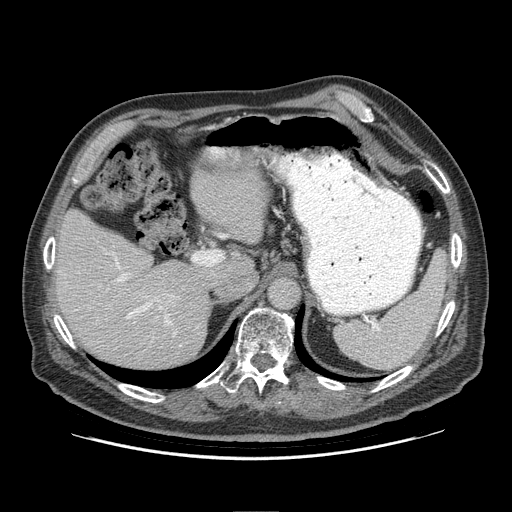
Contrast-enhanced abdominal CT (liver protocol), one axial slice; slice 62 of 95 in the series (ordered by position); reconstruction kernel STANDARD; 140 kVp; soft-tissue window (W 400 / L 40 HU); 512 × 512 image matrix. Case-level facts recorded for this patient, not image findings: diagnosis: hepatocellular carcinoma (patient treated with transarterial chemoembolisation; whether this scan precedes or follows treatment is not stated here); TNM stage (as recorded): Stage-IVB; Child-Pugh class: A; tumour differentiation: well differentiated.
Annotated regions visible in this slice (semi-automatic segmentation, software-assisted and operator-edited):
- liver parenchyma outside the tumour (the mass and vessels are separate outlines, so this box may not span the whole liver): box from (x=54, y=170) to (x=266, y=368) px
- liver vessels: (x=115, y=258)–(x=176, y=335)